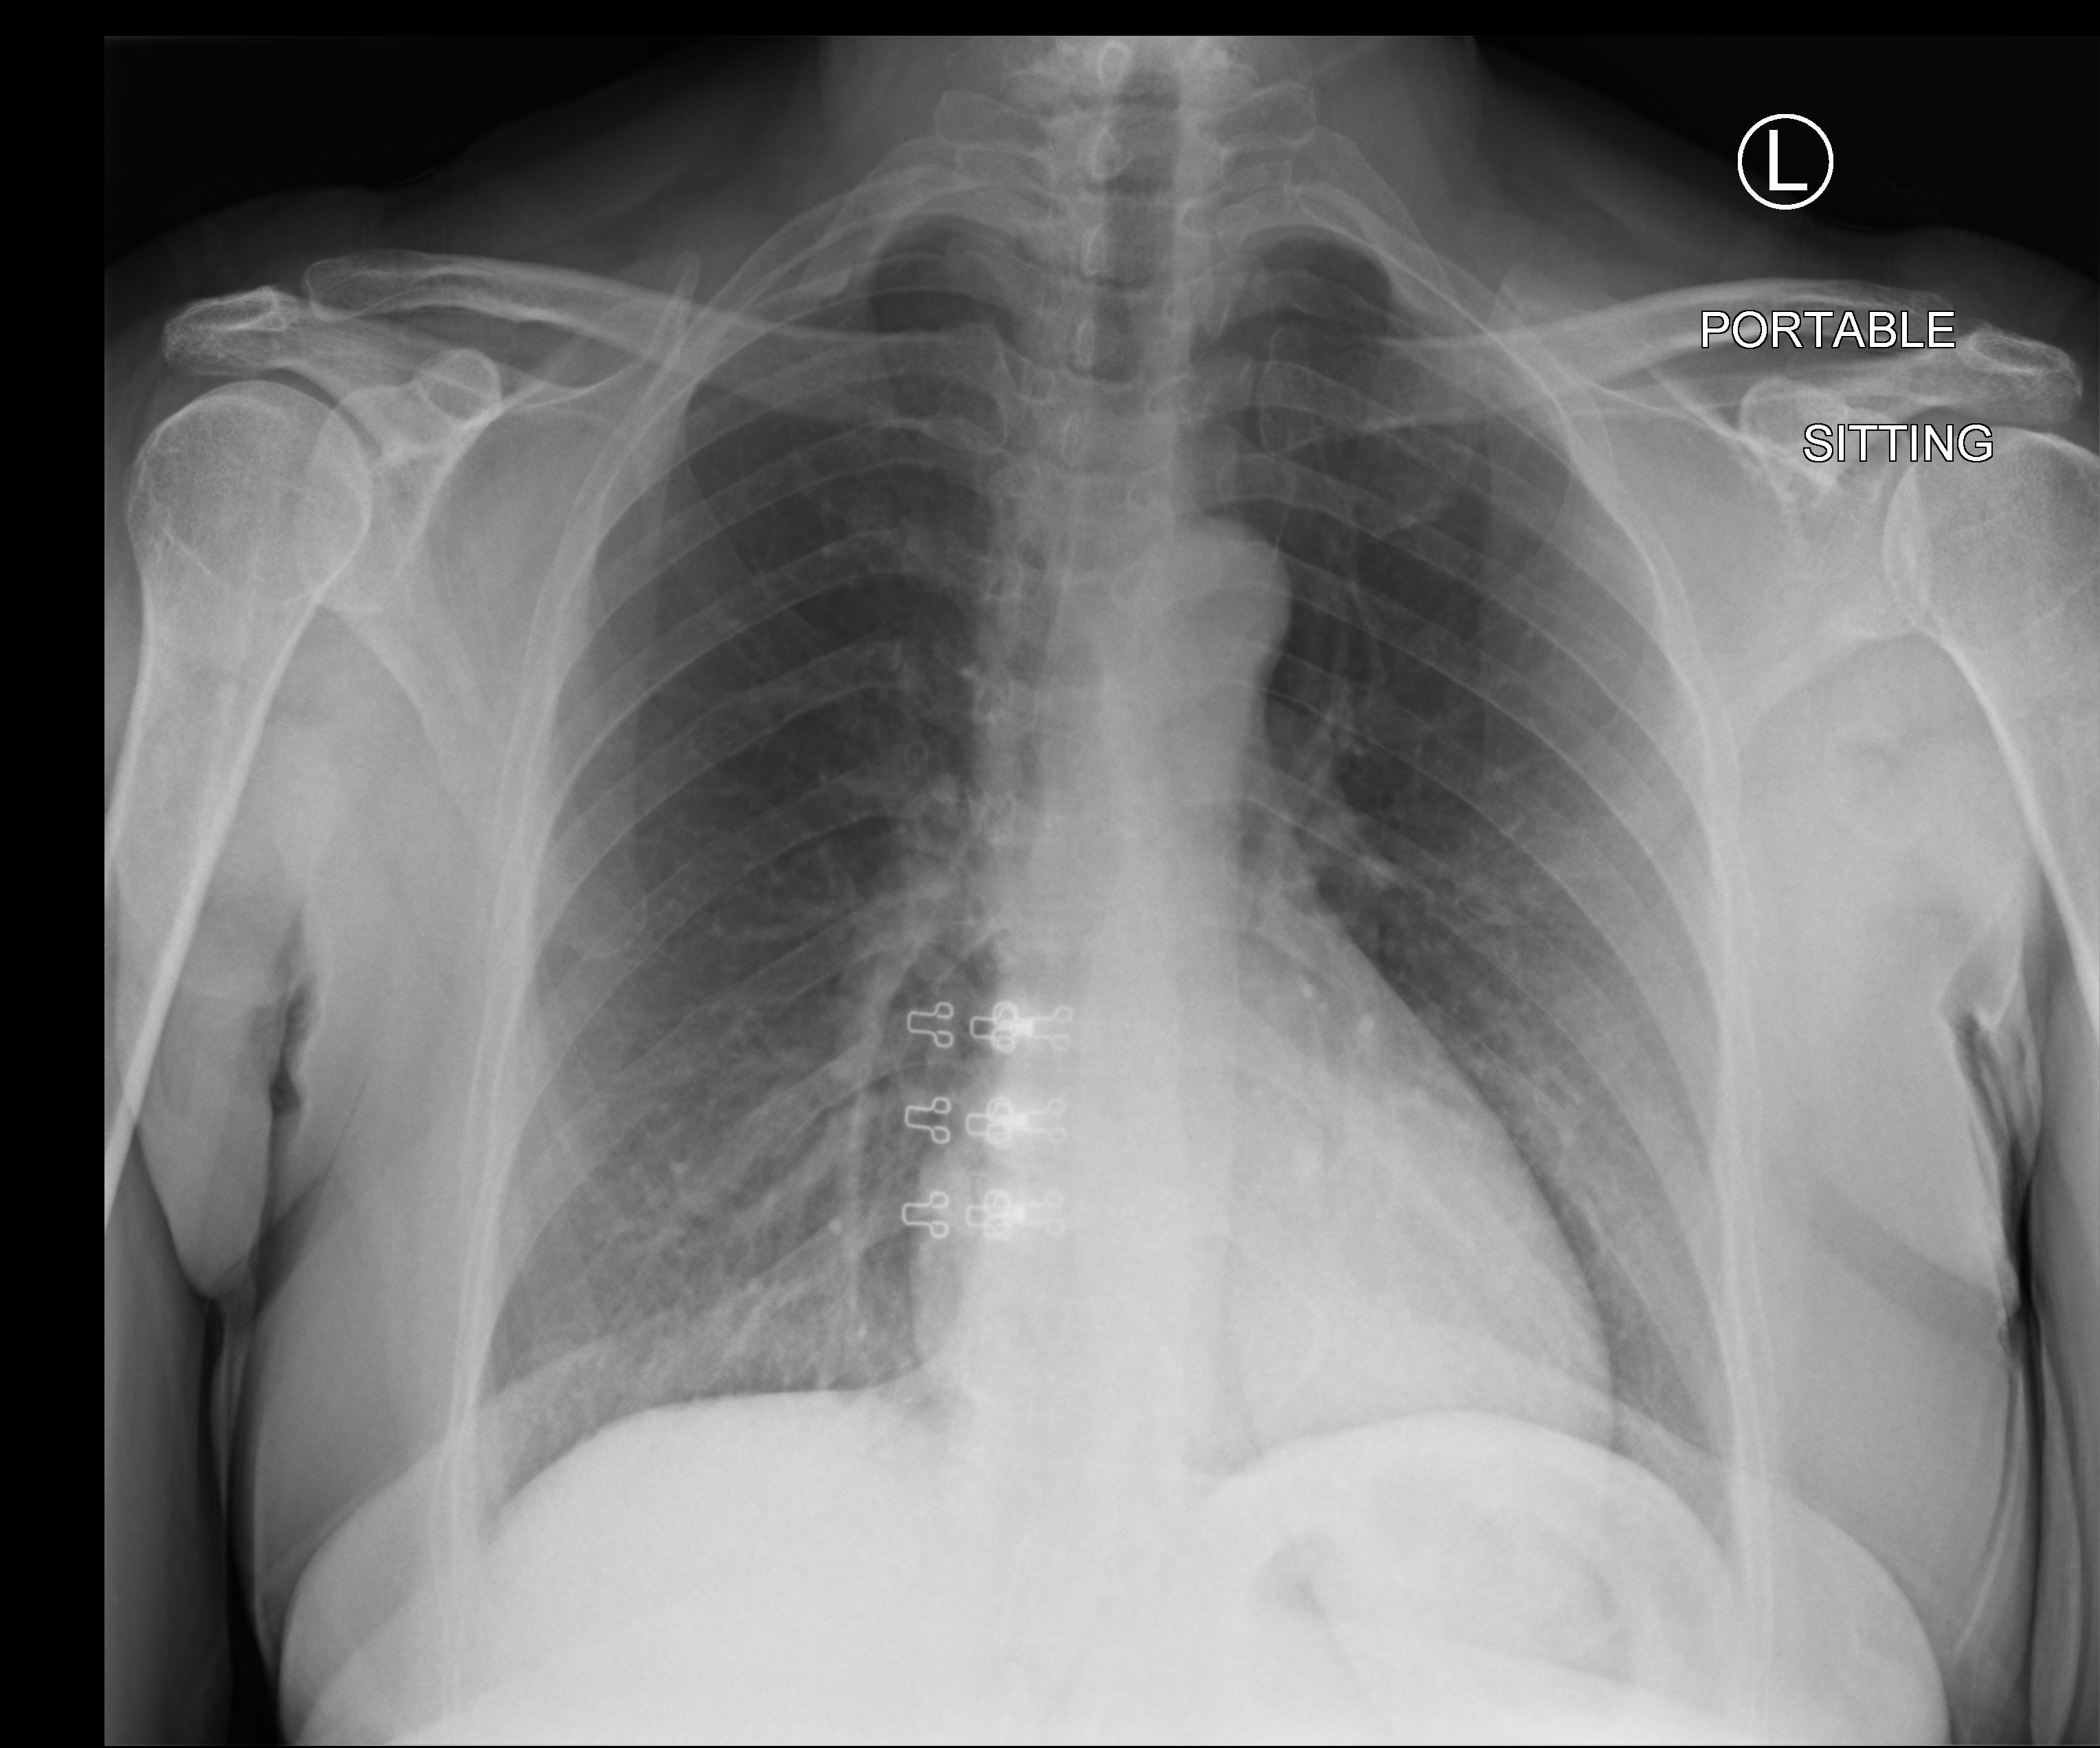
Bedside chest radiograph (computed radiography); anteroposterior (AP) projection. Female patient hospitalised with COVID-19, age 18–59 years.
From the hospital-stay record, not from the radiograph (when in the stay this image was taken is not recorded): admitted to intensive care during this hospital stay: no.